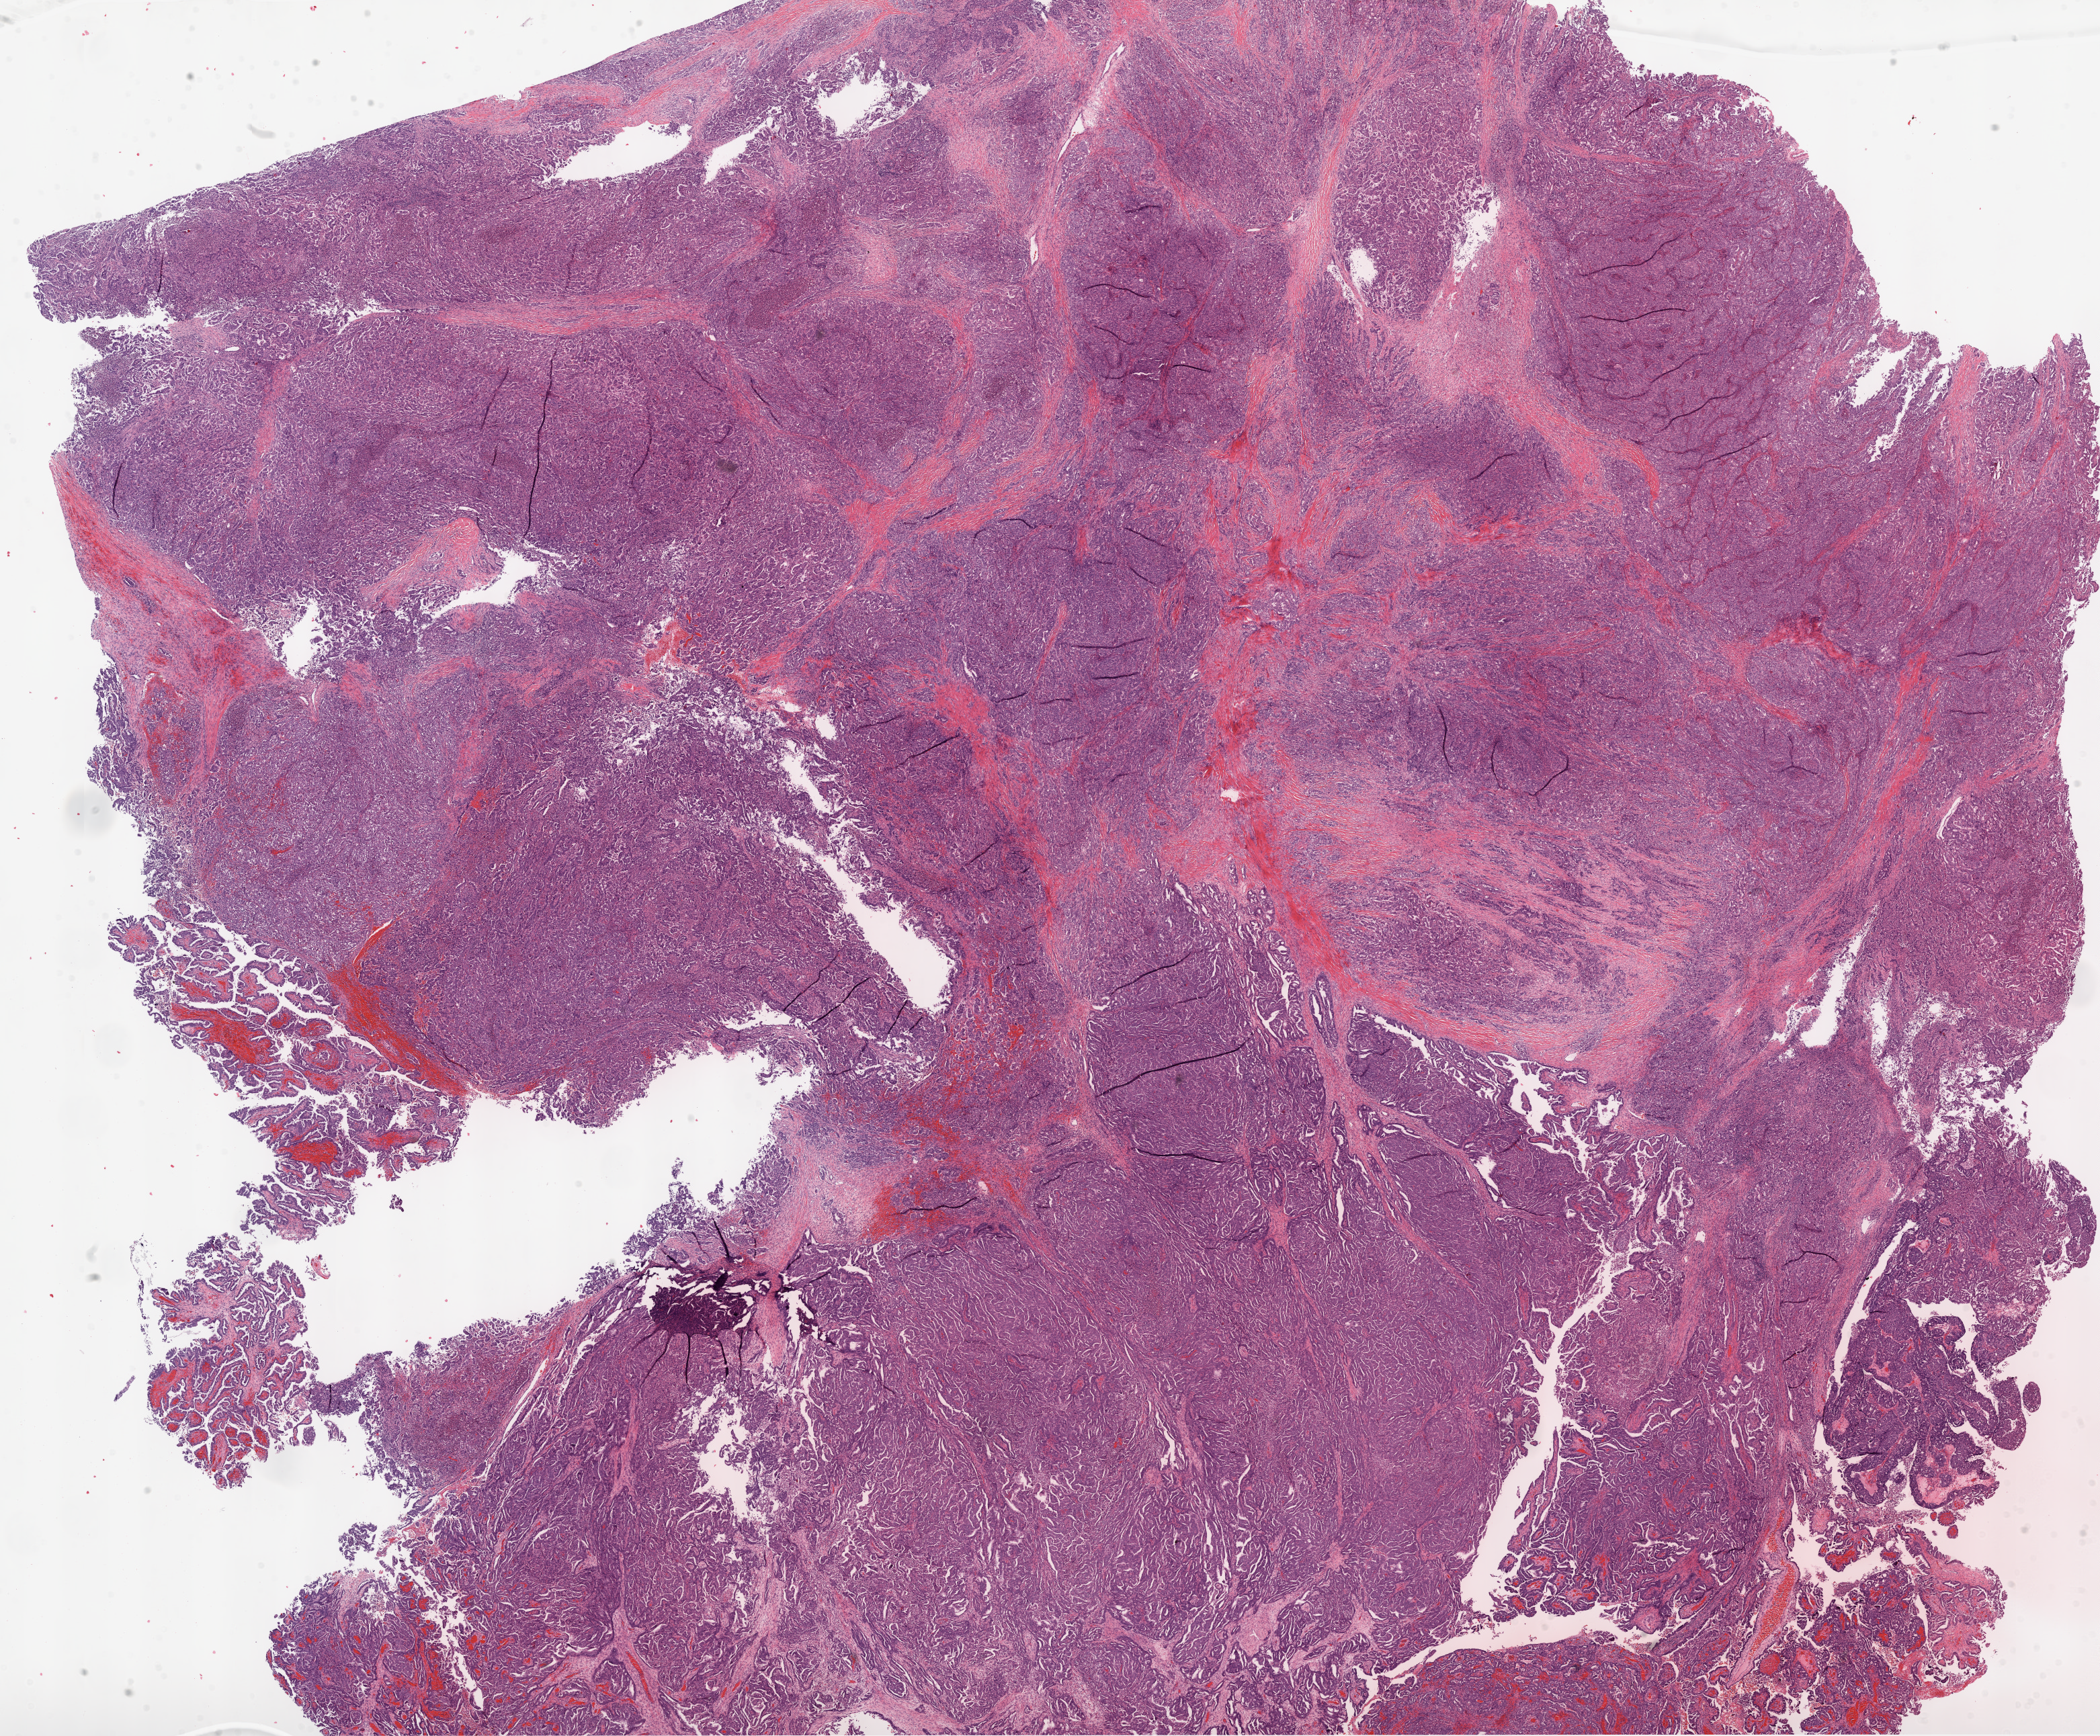
Whole-slide histology image, H&E-stained — shown as a low-resolution overview of the whole scanned area (about 25.1 x 20.7 mm, from a 20x scan), frozen section from the top of the tissue portion, ovary, primary tumour sample. Patient: female, age at initial diagnosis 59 years. Histologic grade: G3 (poorly differentiated). Slide review estimates, as recorded: tumour cells 77%, tumour nuclei 90%, normal cells 0%, stromal cells 20%, necrosis 3%.
FIGO stage: IIIB. Diagnosis: Serous cystadenocarcinoma, NOS.